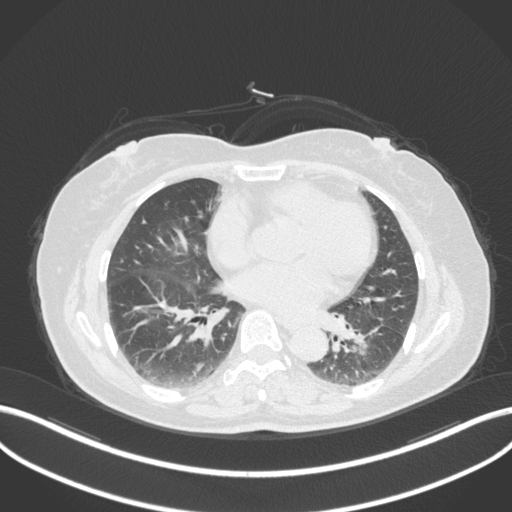
Chest CT, one axial slice. Position 165 of 307 along the scan axis. Reconstruction kernel B31f. 120 kVp. Lung window (W 1500 / L -600 HU). 1 mm slice thickness. 512 × 512 image matrix, field of view 400 × 400 mm. Patient: female, 59 years. Case-level facts recorded for this patient, not image findings: clinical TNM (as recorded): T2a N0 M0.
Structures marked on this image (bounding box drawn by a radiologist):
- lung tumour (recorded histology: adenocarcinoma): bounding box <349,318,388,357> (left, top, right, bottom; pixels)